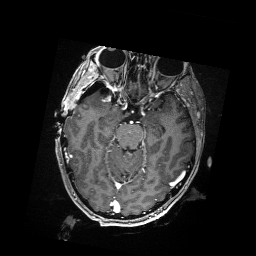
Brain MRI from a brain-tumour surgery series, one axial slice; position 112 of 176 along the scan axis; T1-weighted post-contrast; 1 mm slice thickness; 256 × 256 image matrix. Case-level facts recorded for this patient, not image findings: histopathology: Metastatic Carcinoma from Breast primary; tumour location: Right Frontal.
Outlined on this slice (manually delineated by an expert):
- residual tumour: bounding box [x1, y1, x2, y2] px = [91, 88, 102, 95]